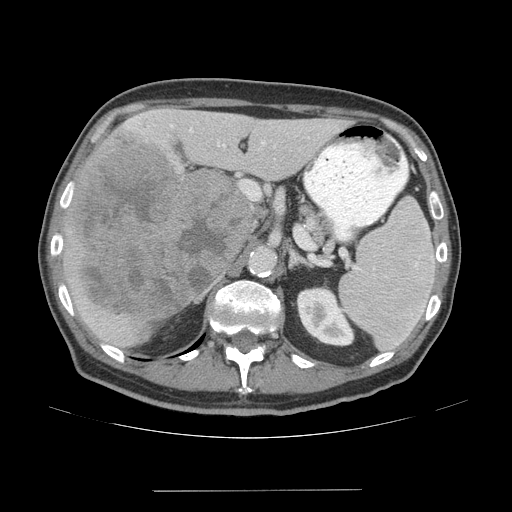
Contrast-enhanced abdominal CT (liver protocol), one axial slice; position 34 of 77 along the scan axis; reconstruction kernel STANDARD; 140 kVp; soft-tissue window (W 400 / L 40 HU); 2.5 mm slice thickness; 512 × 512 image matrix, field of view 400 × 400 mm. From the clinical record (not read from this slice): diagnosis: hepatocellular carcinoma (patient treated with transarterial chemoembolisation; whether this scan precedes or follows treatment is not stated here); TNM stage (as recorded): Stage-IVA; Child-Pugh class: A; tumour nodularity: uninodular.
Annotated regions visible in this slice (semi-automatically segmented with operator editing):
- liver parenchyma outside the tumour (the mass and vessels are separate outlines, so this box may not span the whole liver): bounding box [x1, y1, x2, y2] px = [62, 108, 351, 348]
- mass: [65, 131, 255, 318]
- liver vessels: [128, 119, 281, 208]